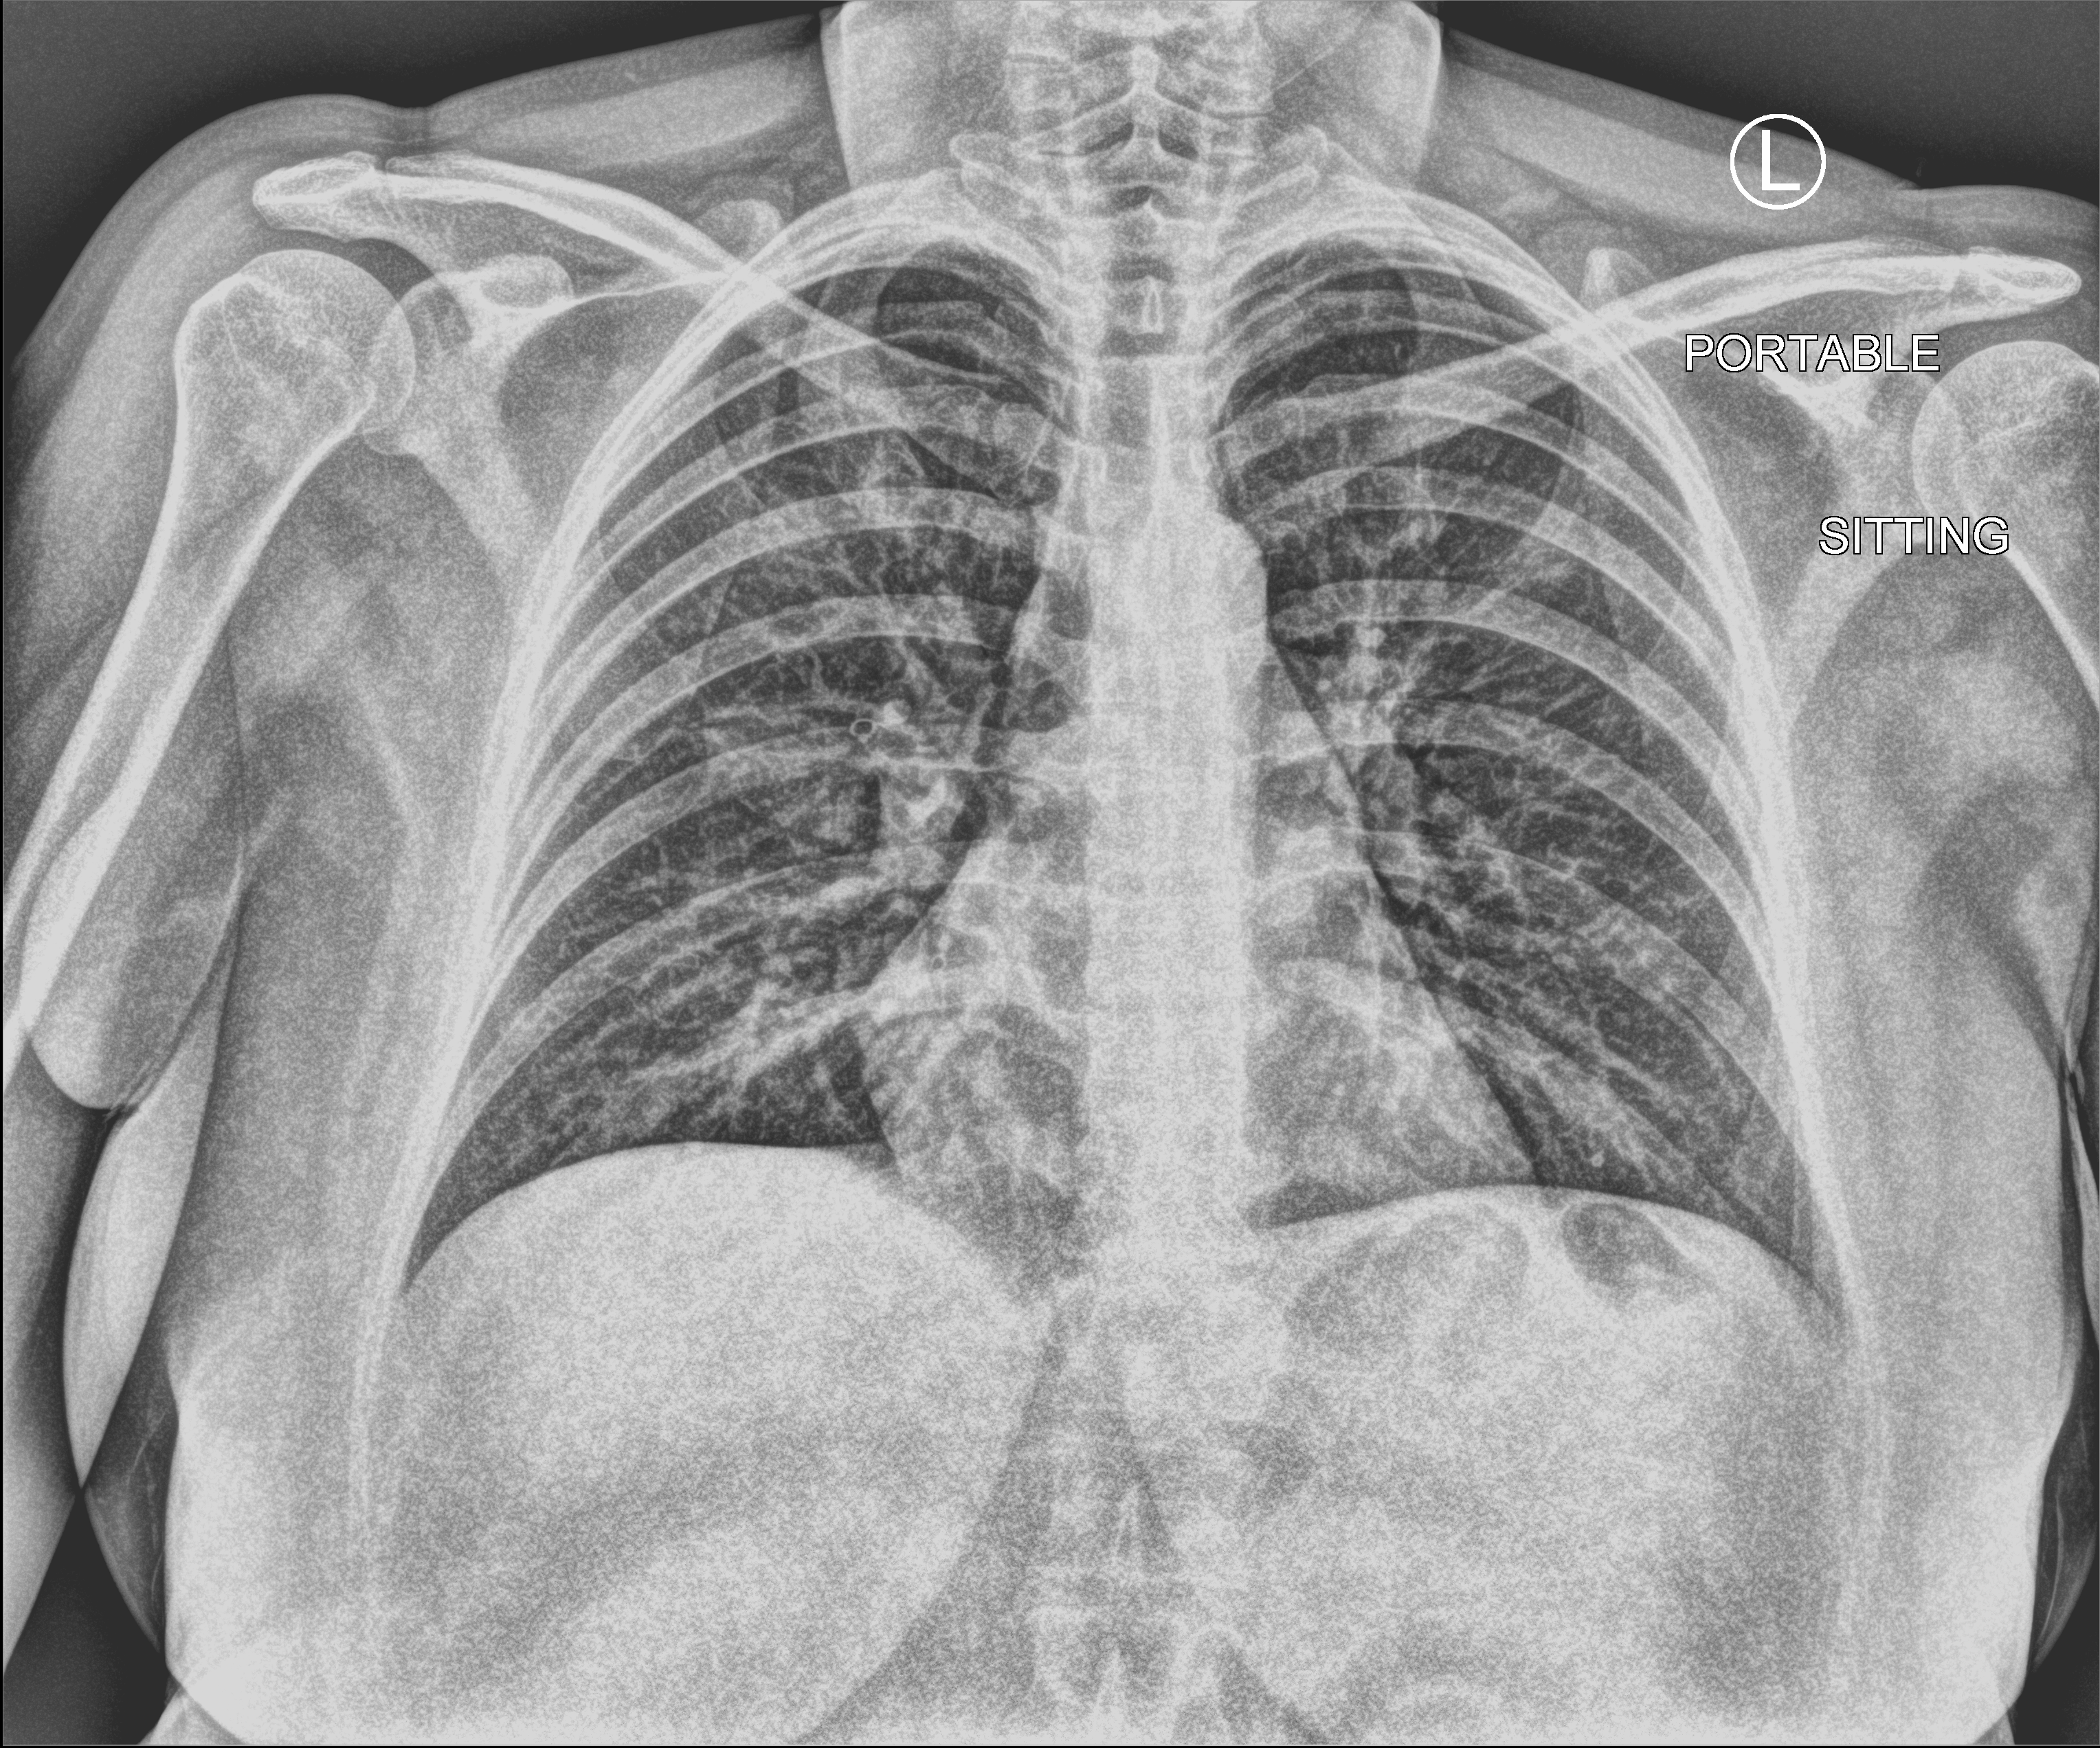
Chest X-ray (portable). Patient hospitalised with COVID-19; female, aged 18–59 years.
Hospital-stay facts (about this admission, not read from this image; timing relative to this image not recorded): mechanically ventilated during this hospital stay: no.